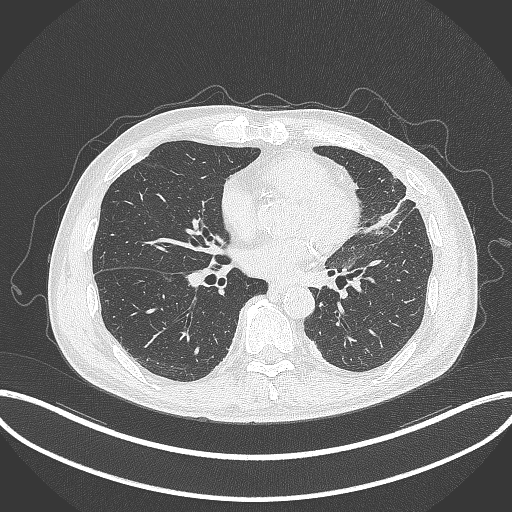
Chest CT, one axial slice. Slice 144 of 382 in the series (ordered by position). 120 kVp. Lung window (W 1500 / L -600 HU). 1 mm slice thickness. 512 × 512 image matrix, field of view 415 × 415 mm. Patient: male, 64 years. Case-level facts recorded for this patient, not image findings: clinical TNM (as recorded): T4 N1 M0.
Outlined on this slice (bounding box drawn by a radiologist):
- lung tumour (recorded histology: adenocarcinoma): bounding box <360,192,416,239> (left, top, right, bottom; pixels)